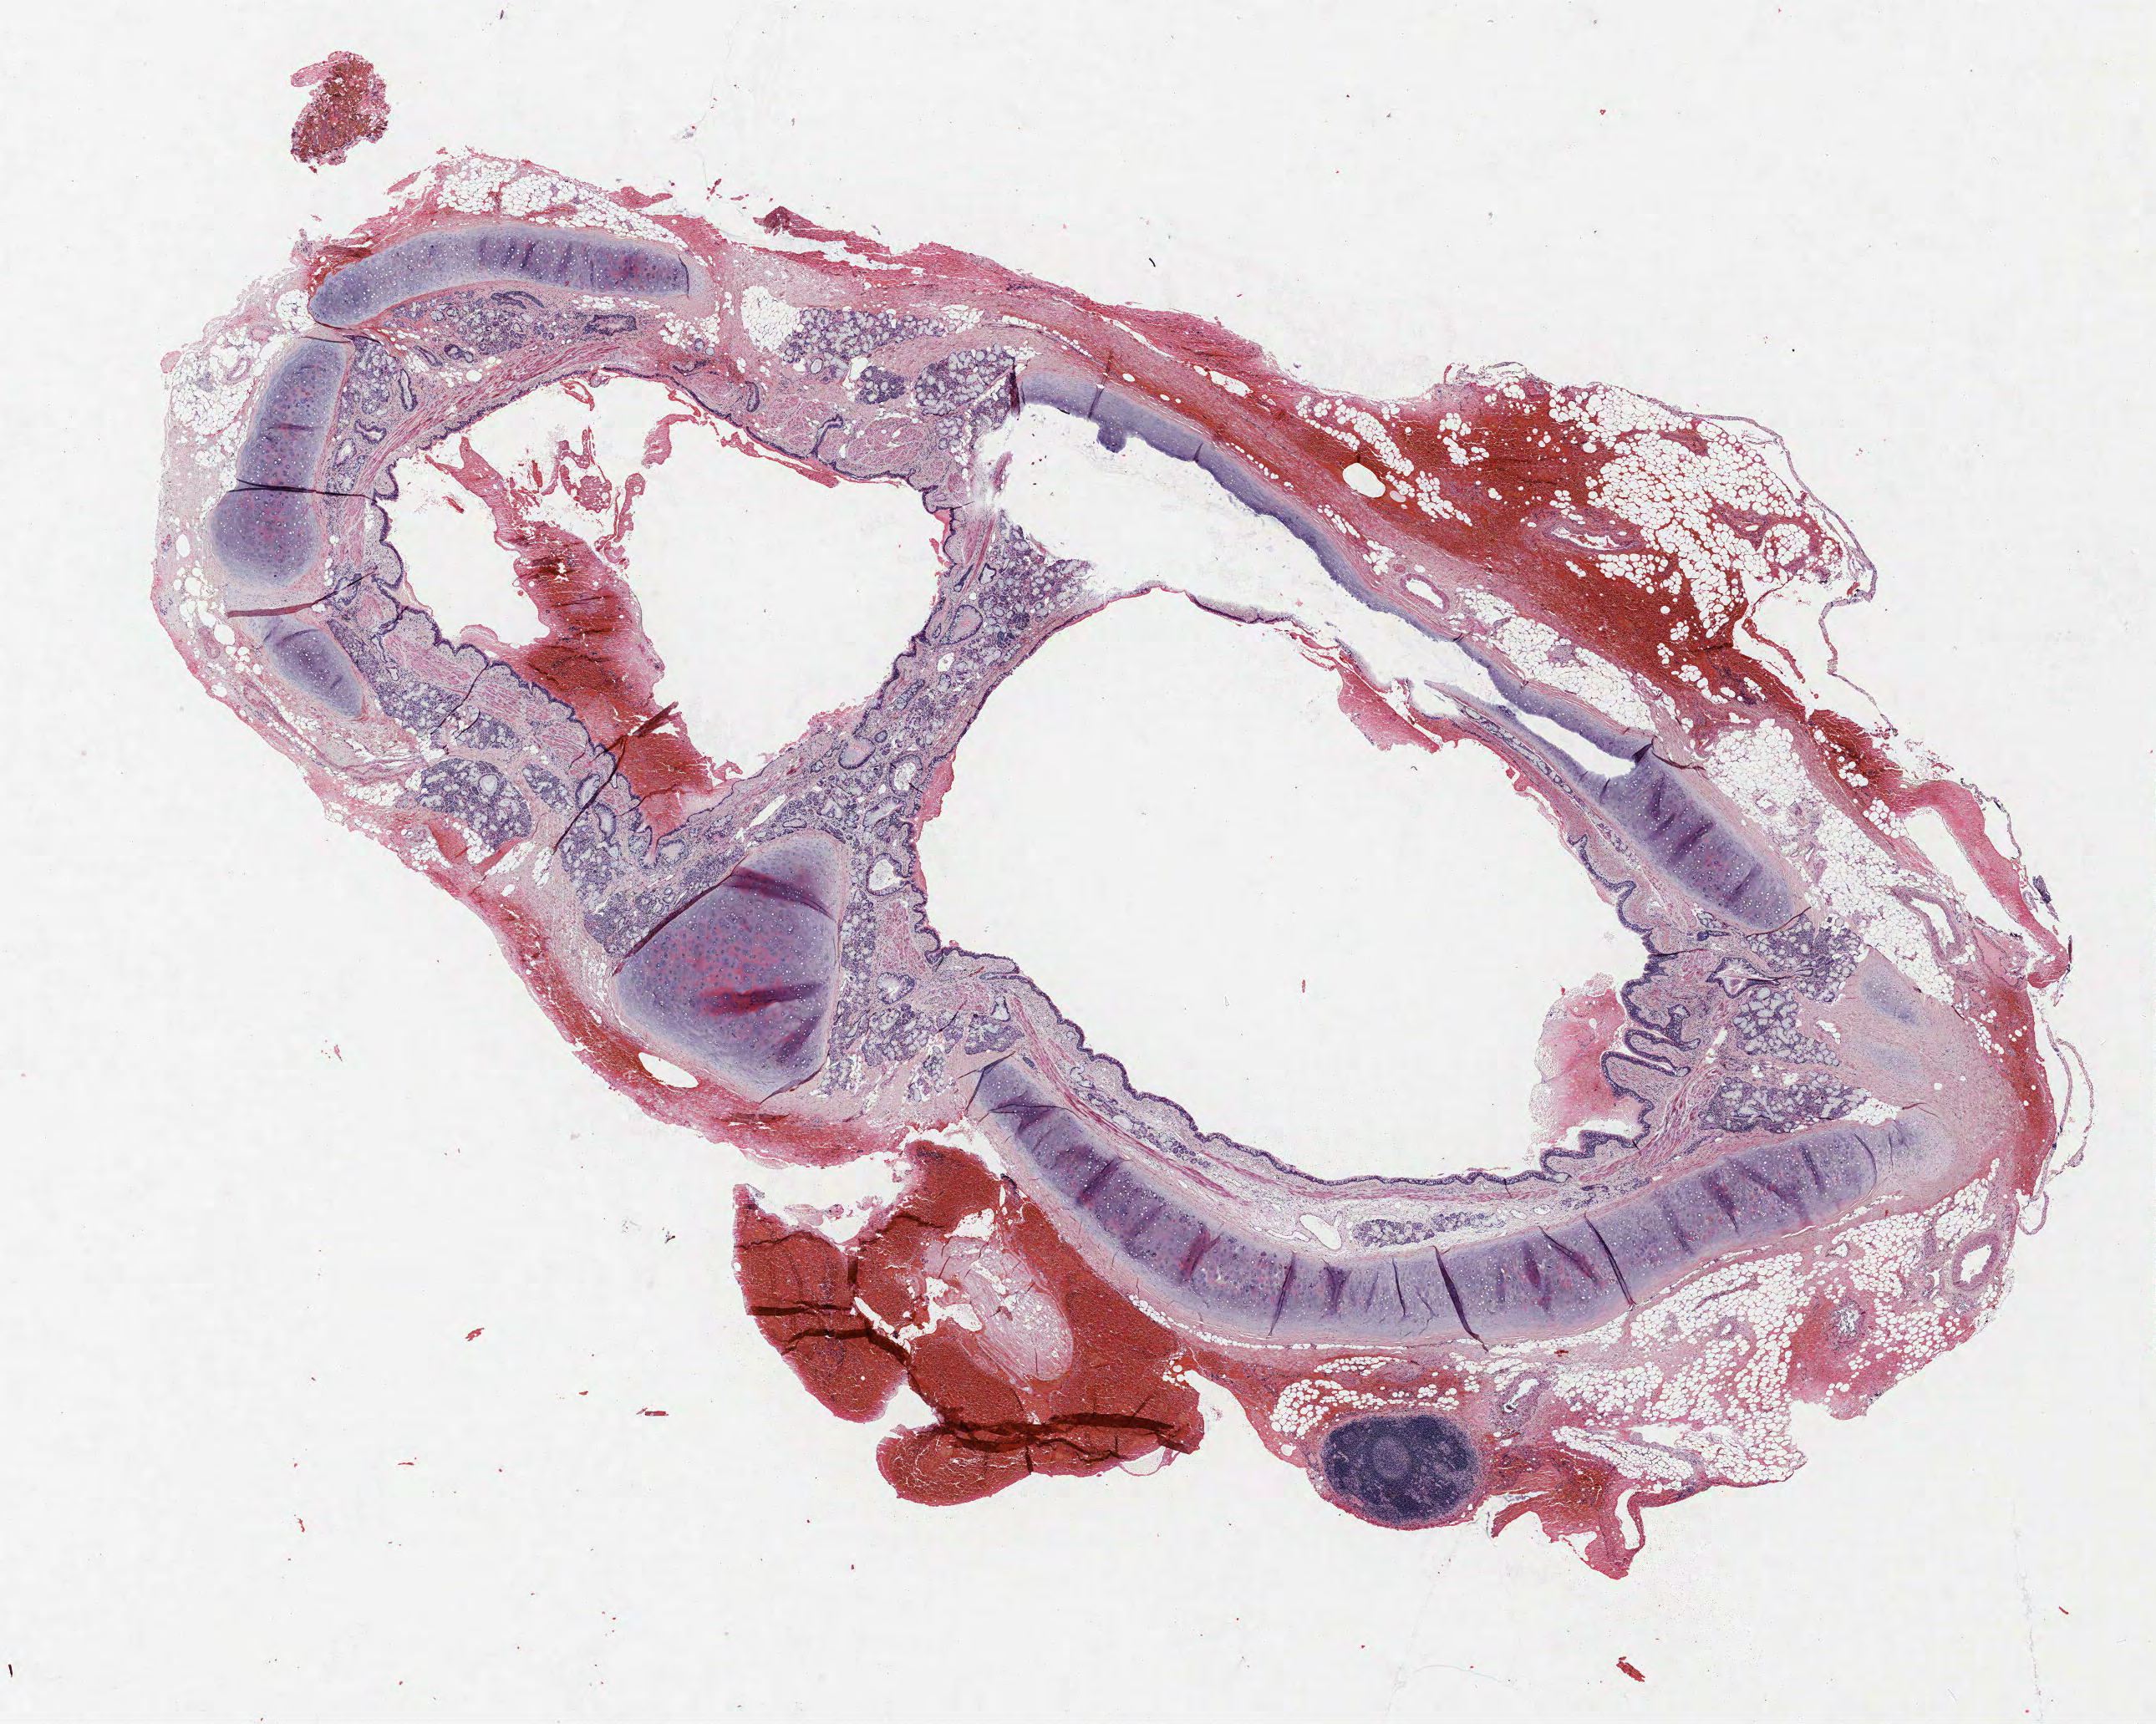
Whole-slide histology image, H&E — whole scanned area (about 20.6 x 16.5 mm, slide scanned at 40x) shown as a low-resolution overview; formalin-fixed paraffin-embedded (FFPE) section; lung. Male, age 55 at enrolment.
Participant's lung-cancer diagnosis: Large cell neuroendocrine carcinoma. Tumour size (pathology): 15 mm. Primary tumour location (clinical record): left upper lobe. Stage (AJCC 6th edition): IA. ICD-O-3 topography: upper lobe of lung (C34.1).